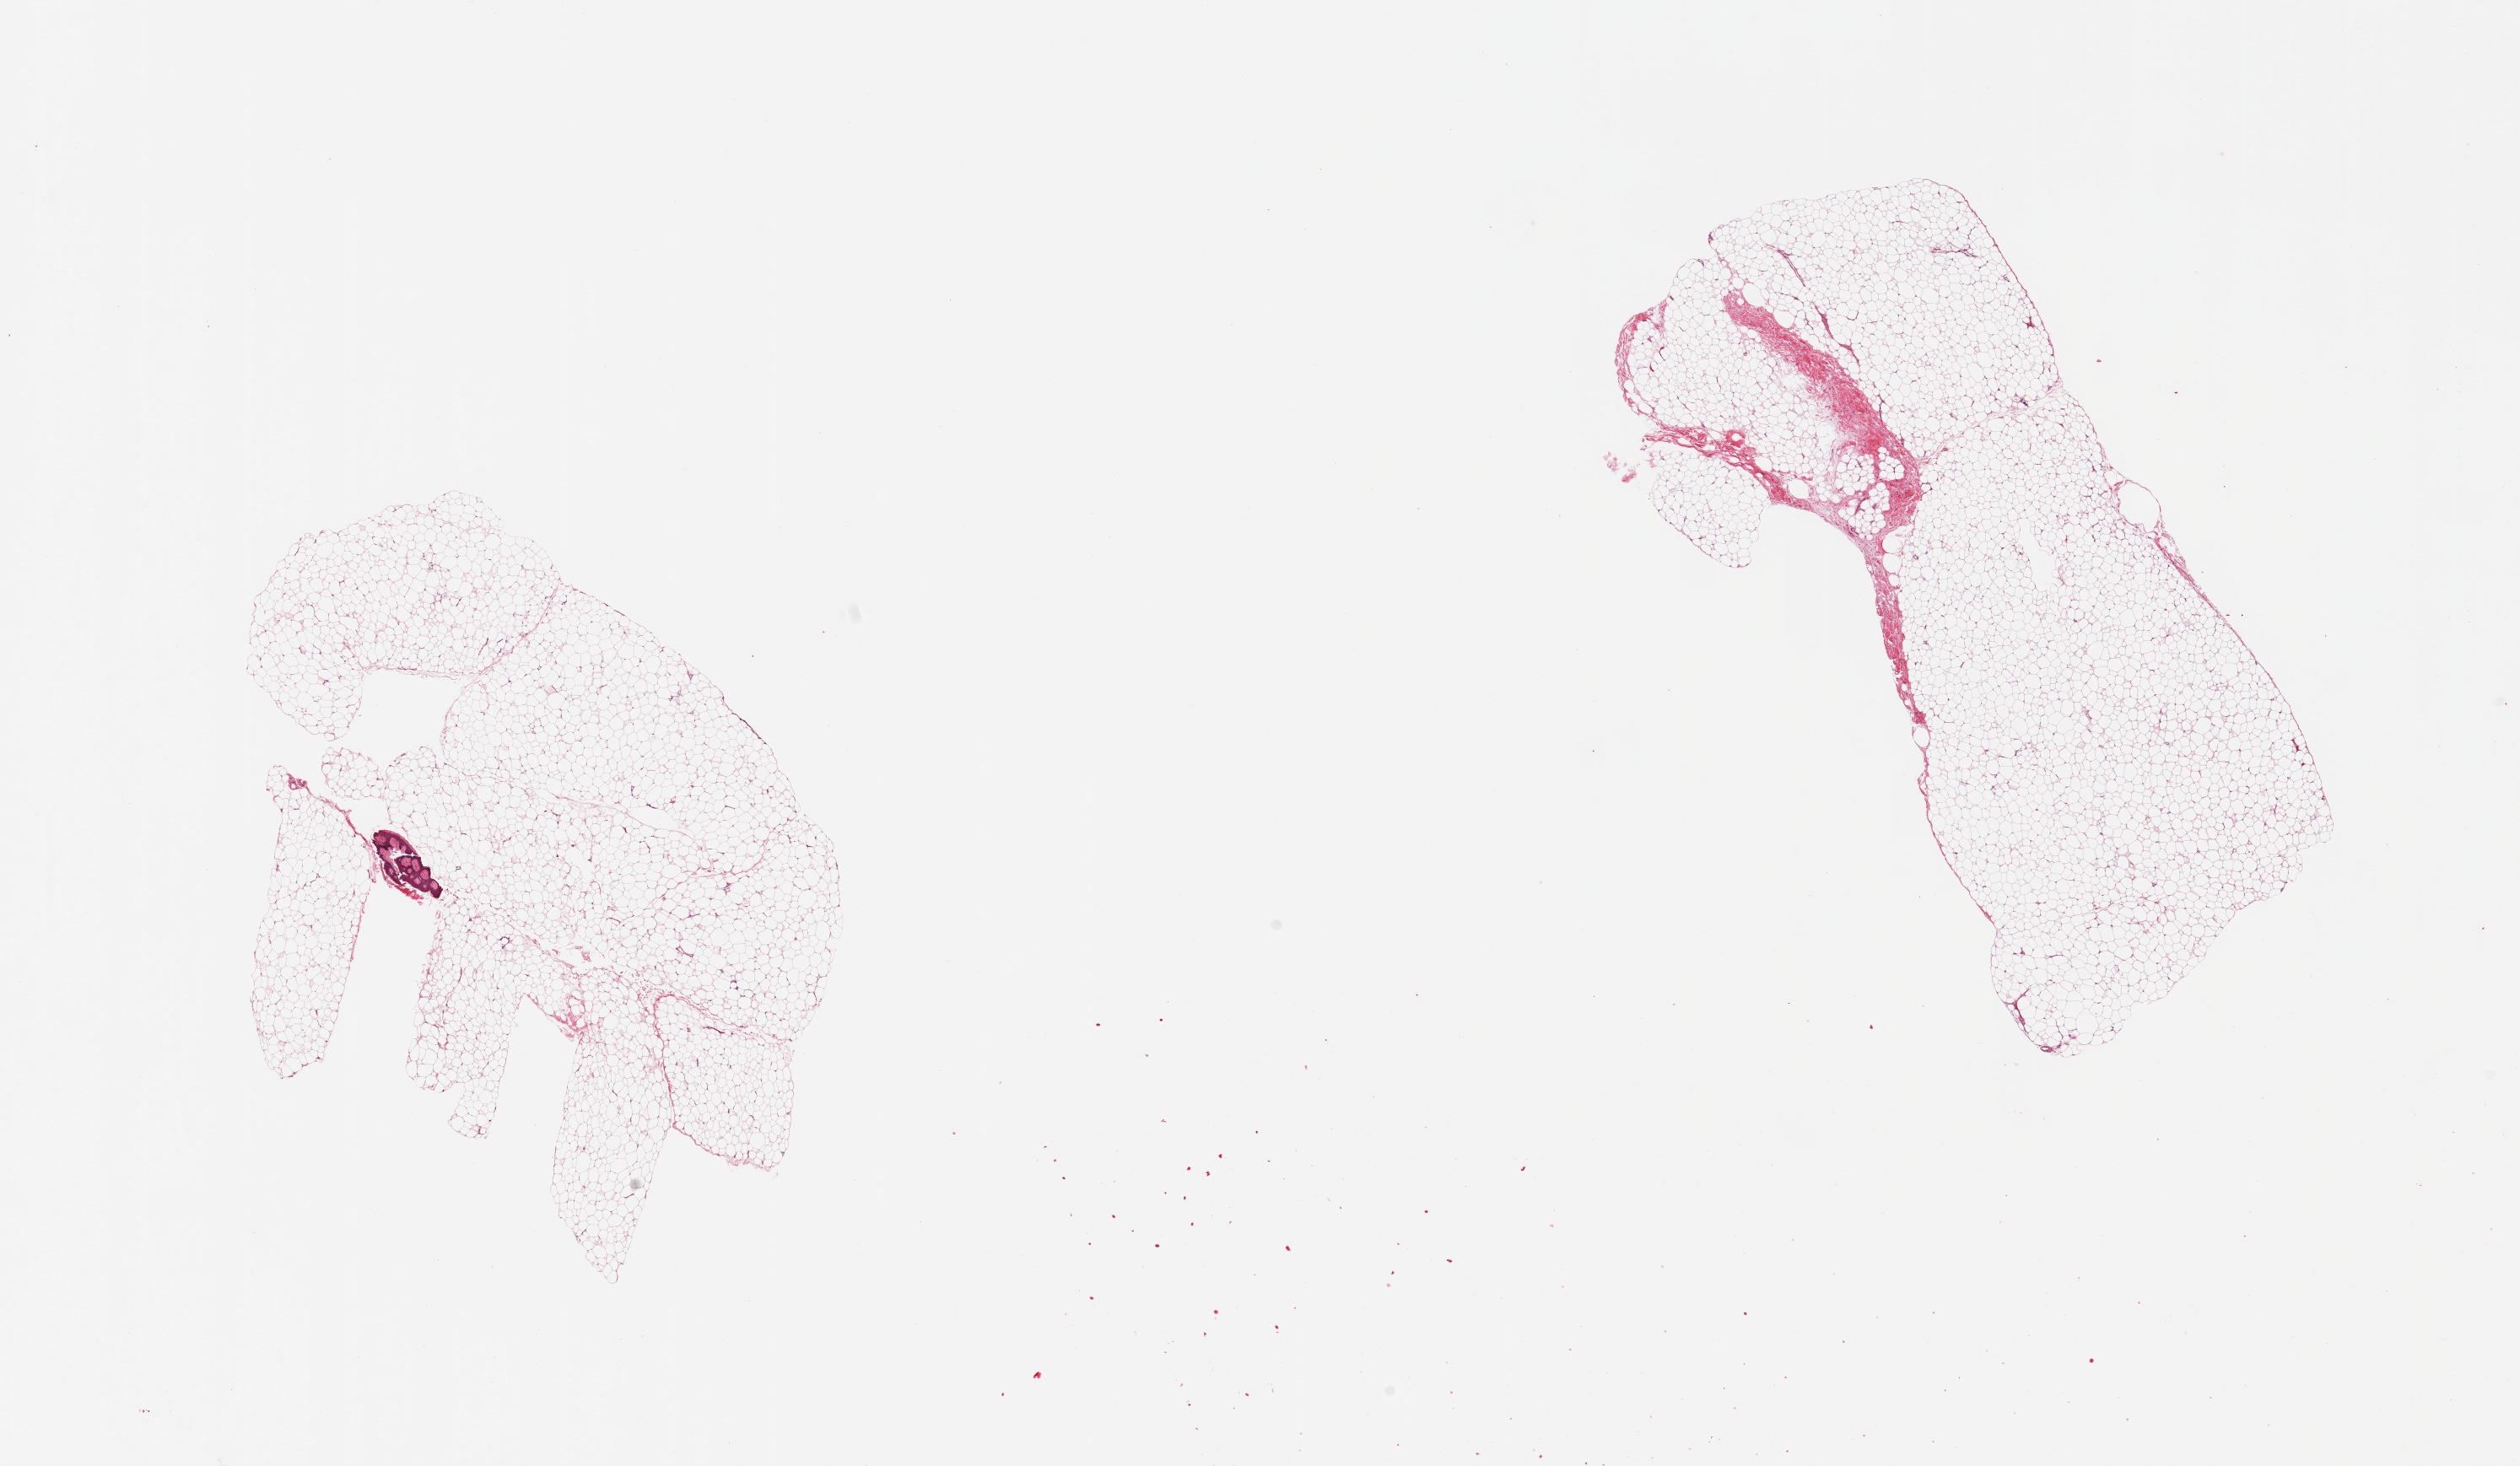
Haematoxylin and eosin whole-slide image, brightfield — shown as a low-resolution overview of the whole scanned area (about 23.6 x 13.7 mm, acquisition: 20x scan), PAXgene-fixed, paraffin-embedded tissue, section of adipose tissue (target tissue), tissue donor sample.
Pathologist's review note for this sample: 2 pieces; adipose tissue and one 0.9 mm squamous epithelium floater.